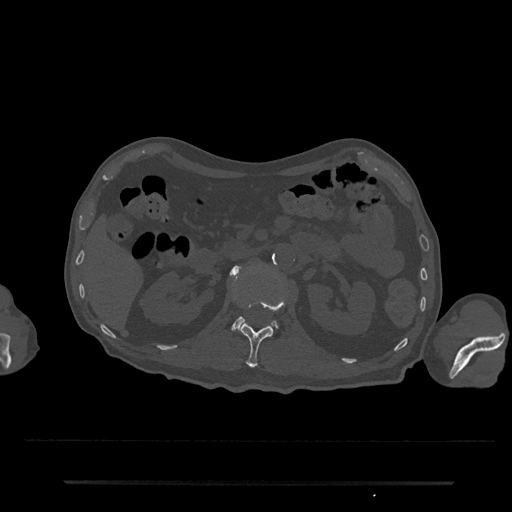
CT including the spine, one axial slice; slice 106 of 797 in the series (ordered by position); reconstruction kernel Br40s/3; 120 kVp; bone window (W 1800 / L 400 HU); 0.5 mm slice thickness; 512 × 512 image matrix, field of view 427 × 427 mm. Male patient, age 74 years. From the clinical record (not read from this slice): primary cancer: prostate.
Outlined on this slice (semi-automatically segmented with operator editing):
- L1 vertebra: bounding box <232,293,286,368> (left, top, right, bottom; pixels)
- L2 vertebra: <231,266,277,331>